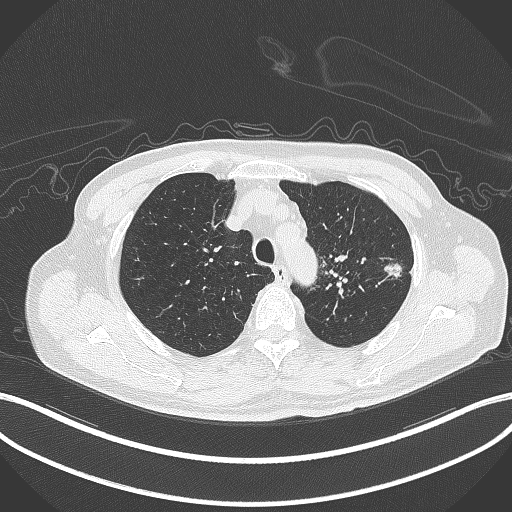
Chest CT, one axial slice; position 349 of 417 along the scan axis; reconstruction kernel B70f; 120 kVp; lung window (W 1500 / L -600 HU); 1 mm slice thickness; 512 × 512 image matrix, field of view 400 × 400 mm. Patient: male, 77 years. From the clinical record (not read from this slice): clinical TNM (as recorded): T3 N1 M0.
Outlined on this slice (rectangle marked by the reading radiologist):
- lung tumour (recorded histology: adenocarcinoma): box from (x=382, y=261) to (x=405, y=279) px